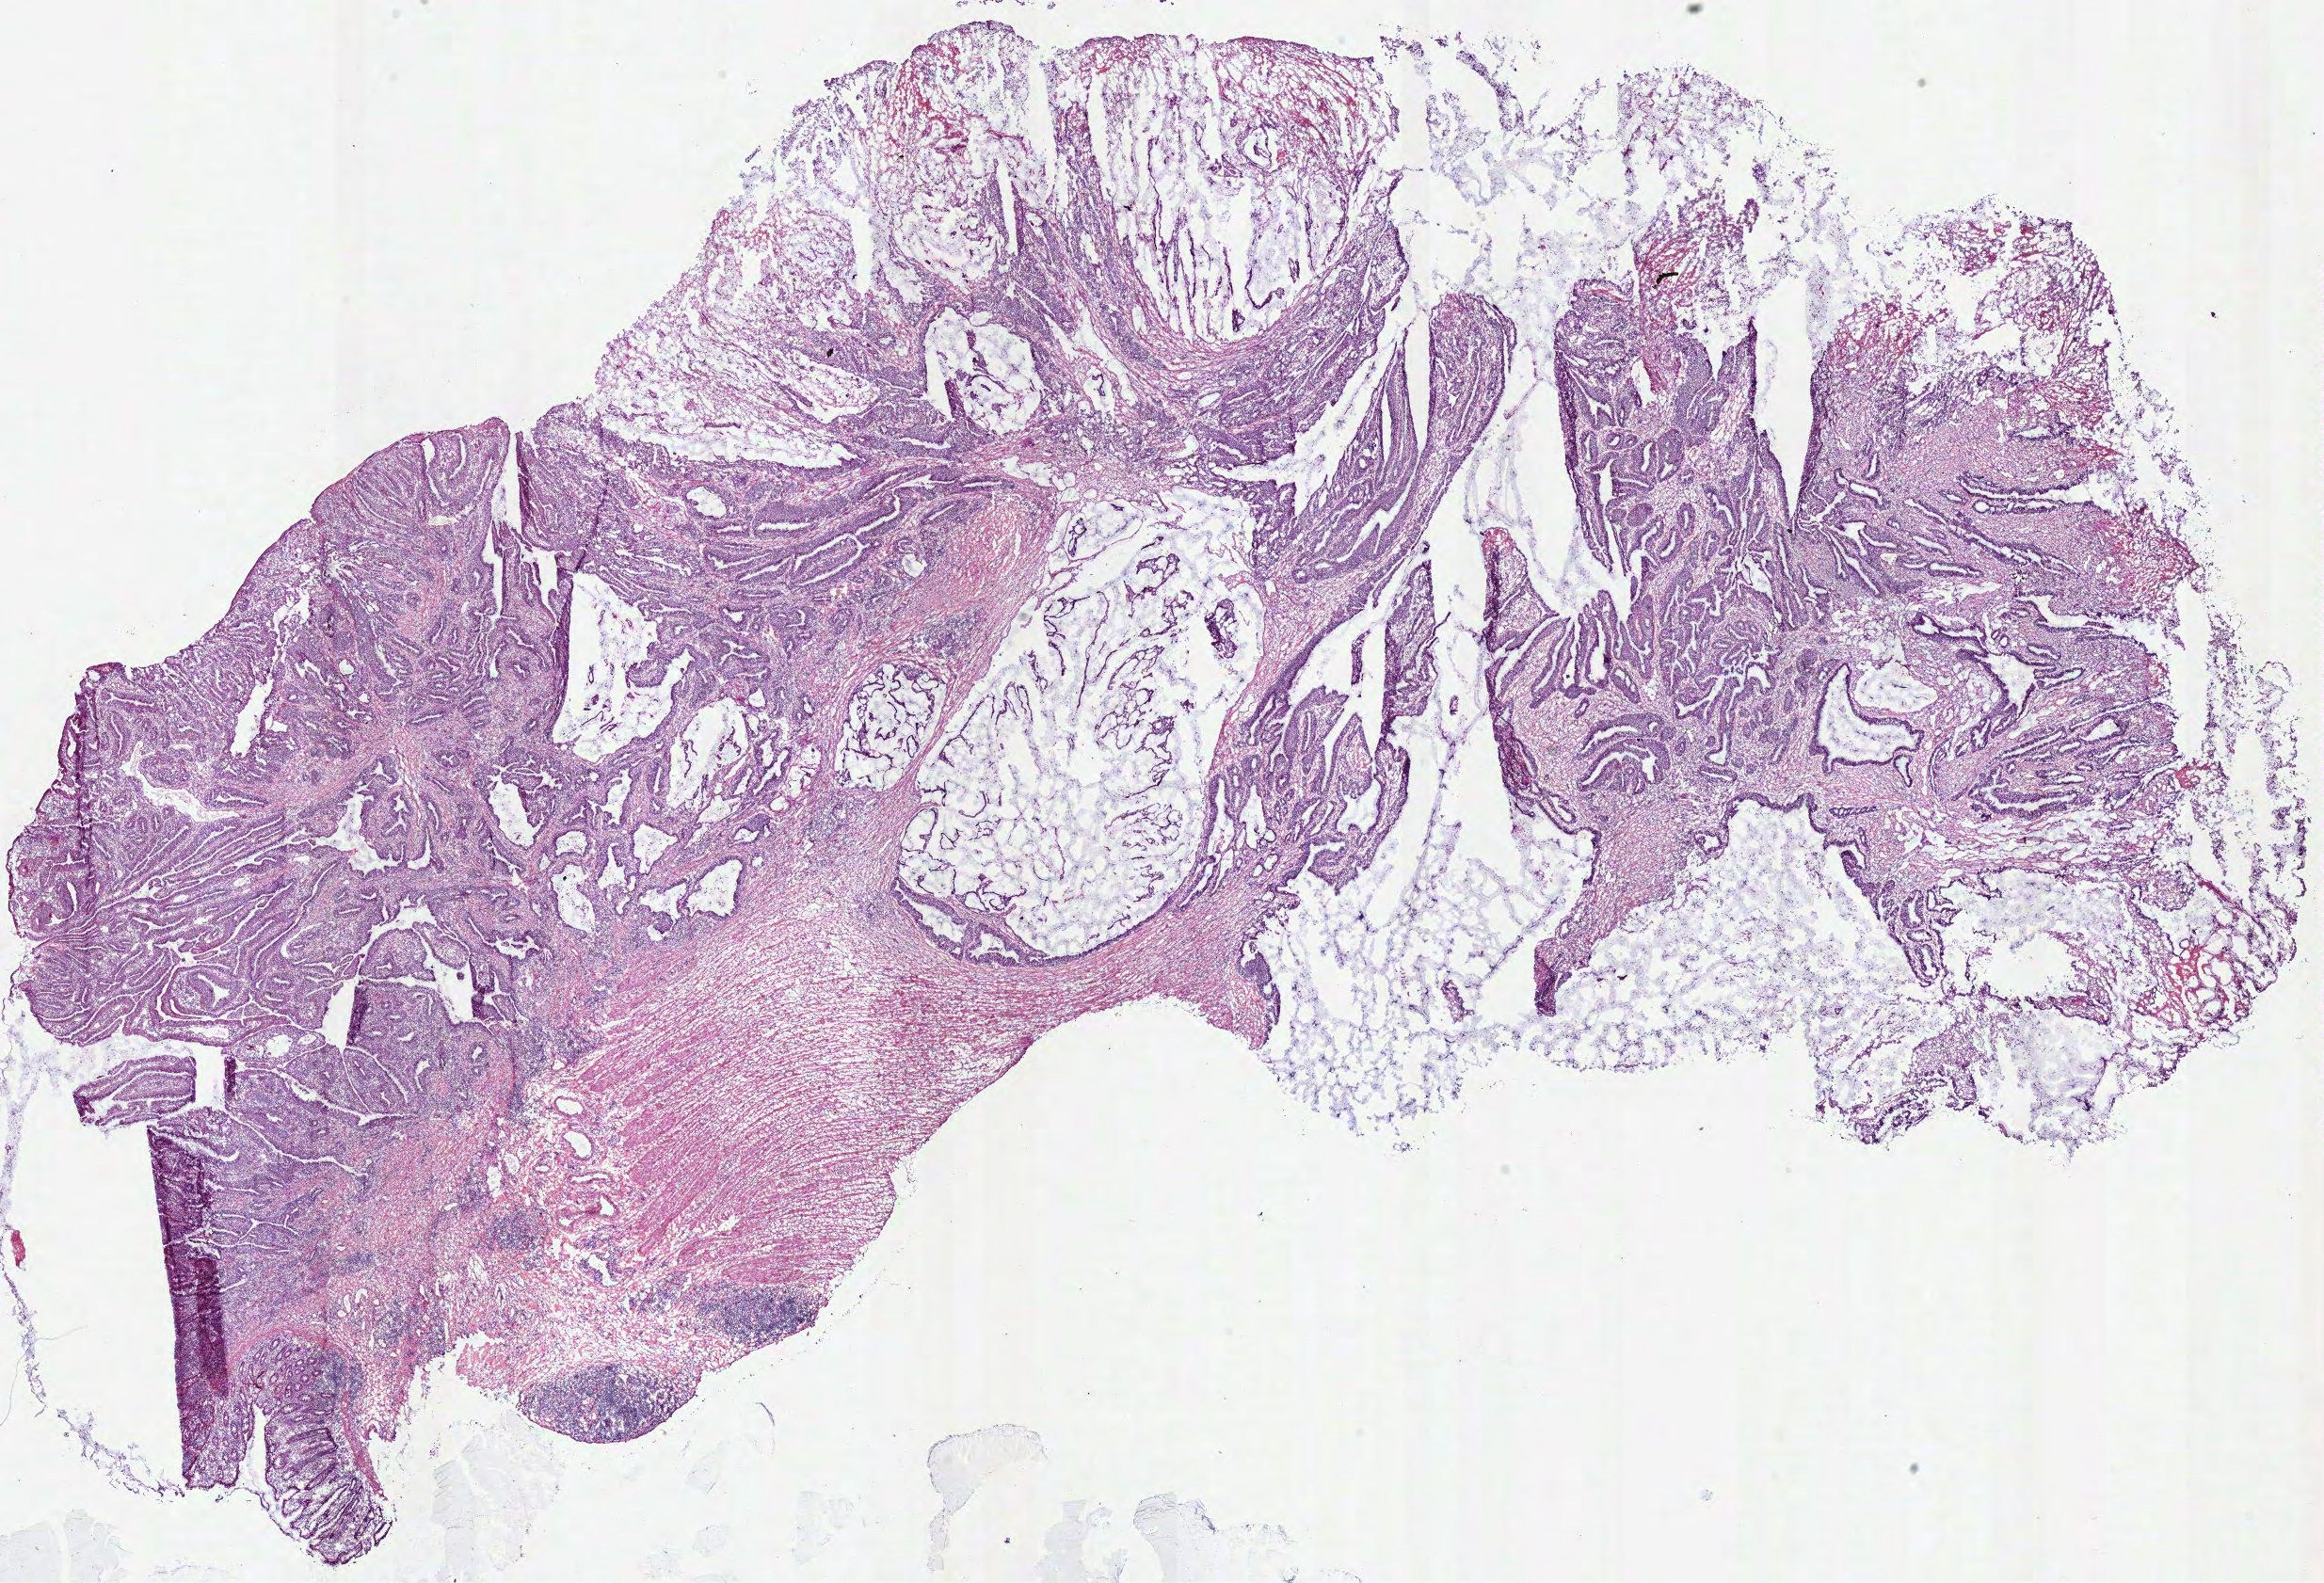
Whole-slide histology image, H&E, whole scanned area (about 19.5 x 13.3 mm) shown as a low-resolution overview; frozen section from the top of the tissue portion; primary tumour sample from the colon. Male, age 45 years at initial diagnosis. Composition of this section per pathologist review: tumour cells 81%, tumour nuclei 80%, normal cells 3%, stromal cells 15%, necrosis 1%.
Pathologic diagnosis: Mucinous adenocarcinoma (cecum). AJCC pathologic stage: I (7th edition). Lymph nodes positive (case pathology): 0 of 21 examined.